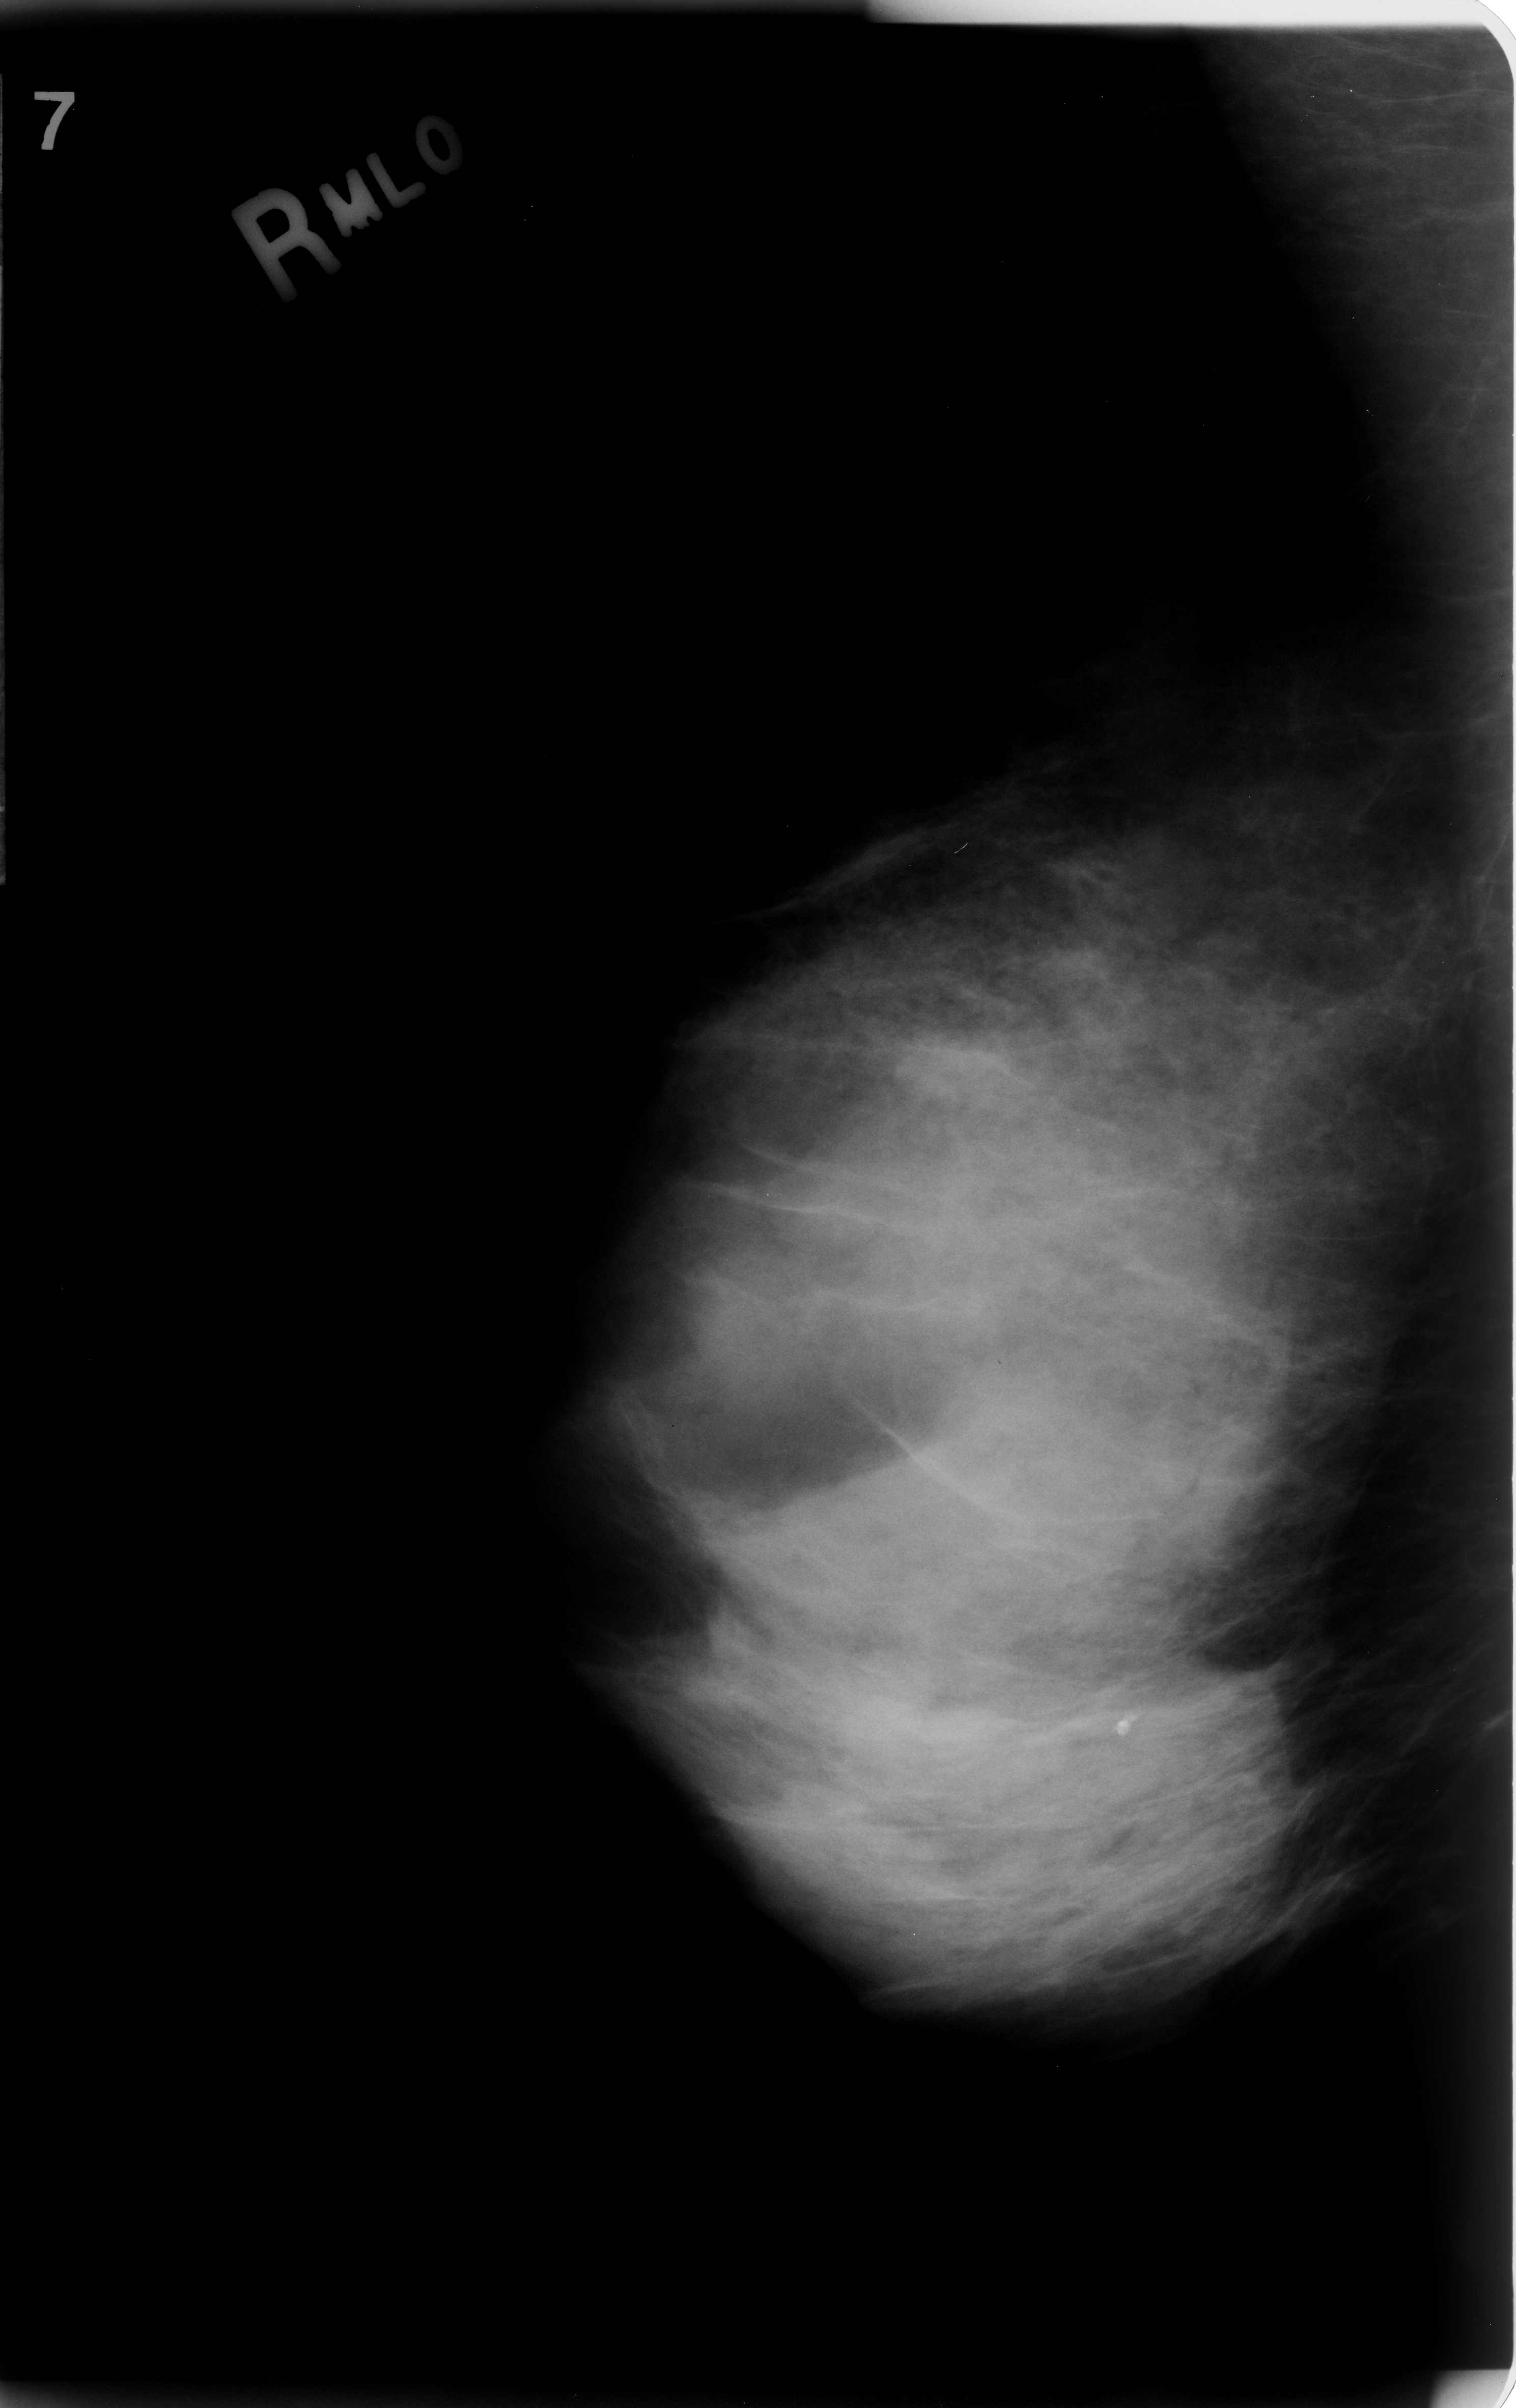
Scanned film-screen mammogram, right breast, mediolateral oblique (MLO) view, breast composition: extremely dense (BI-RADS density category 4 of 4).
Marked abnormality: calcifications, morphology dystrophic, distribution clustered; BI-RADS assessment category 3; pathology (as recorded): benign.